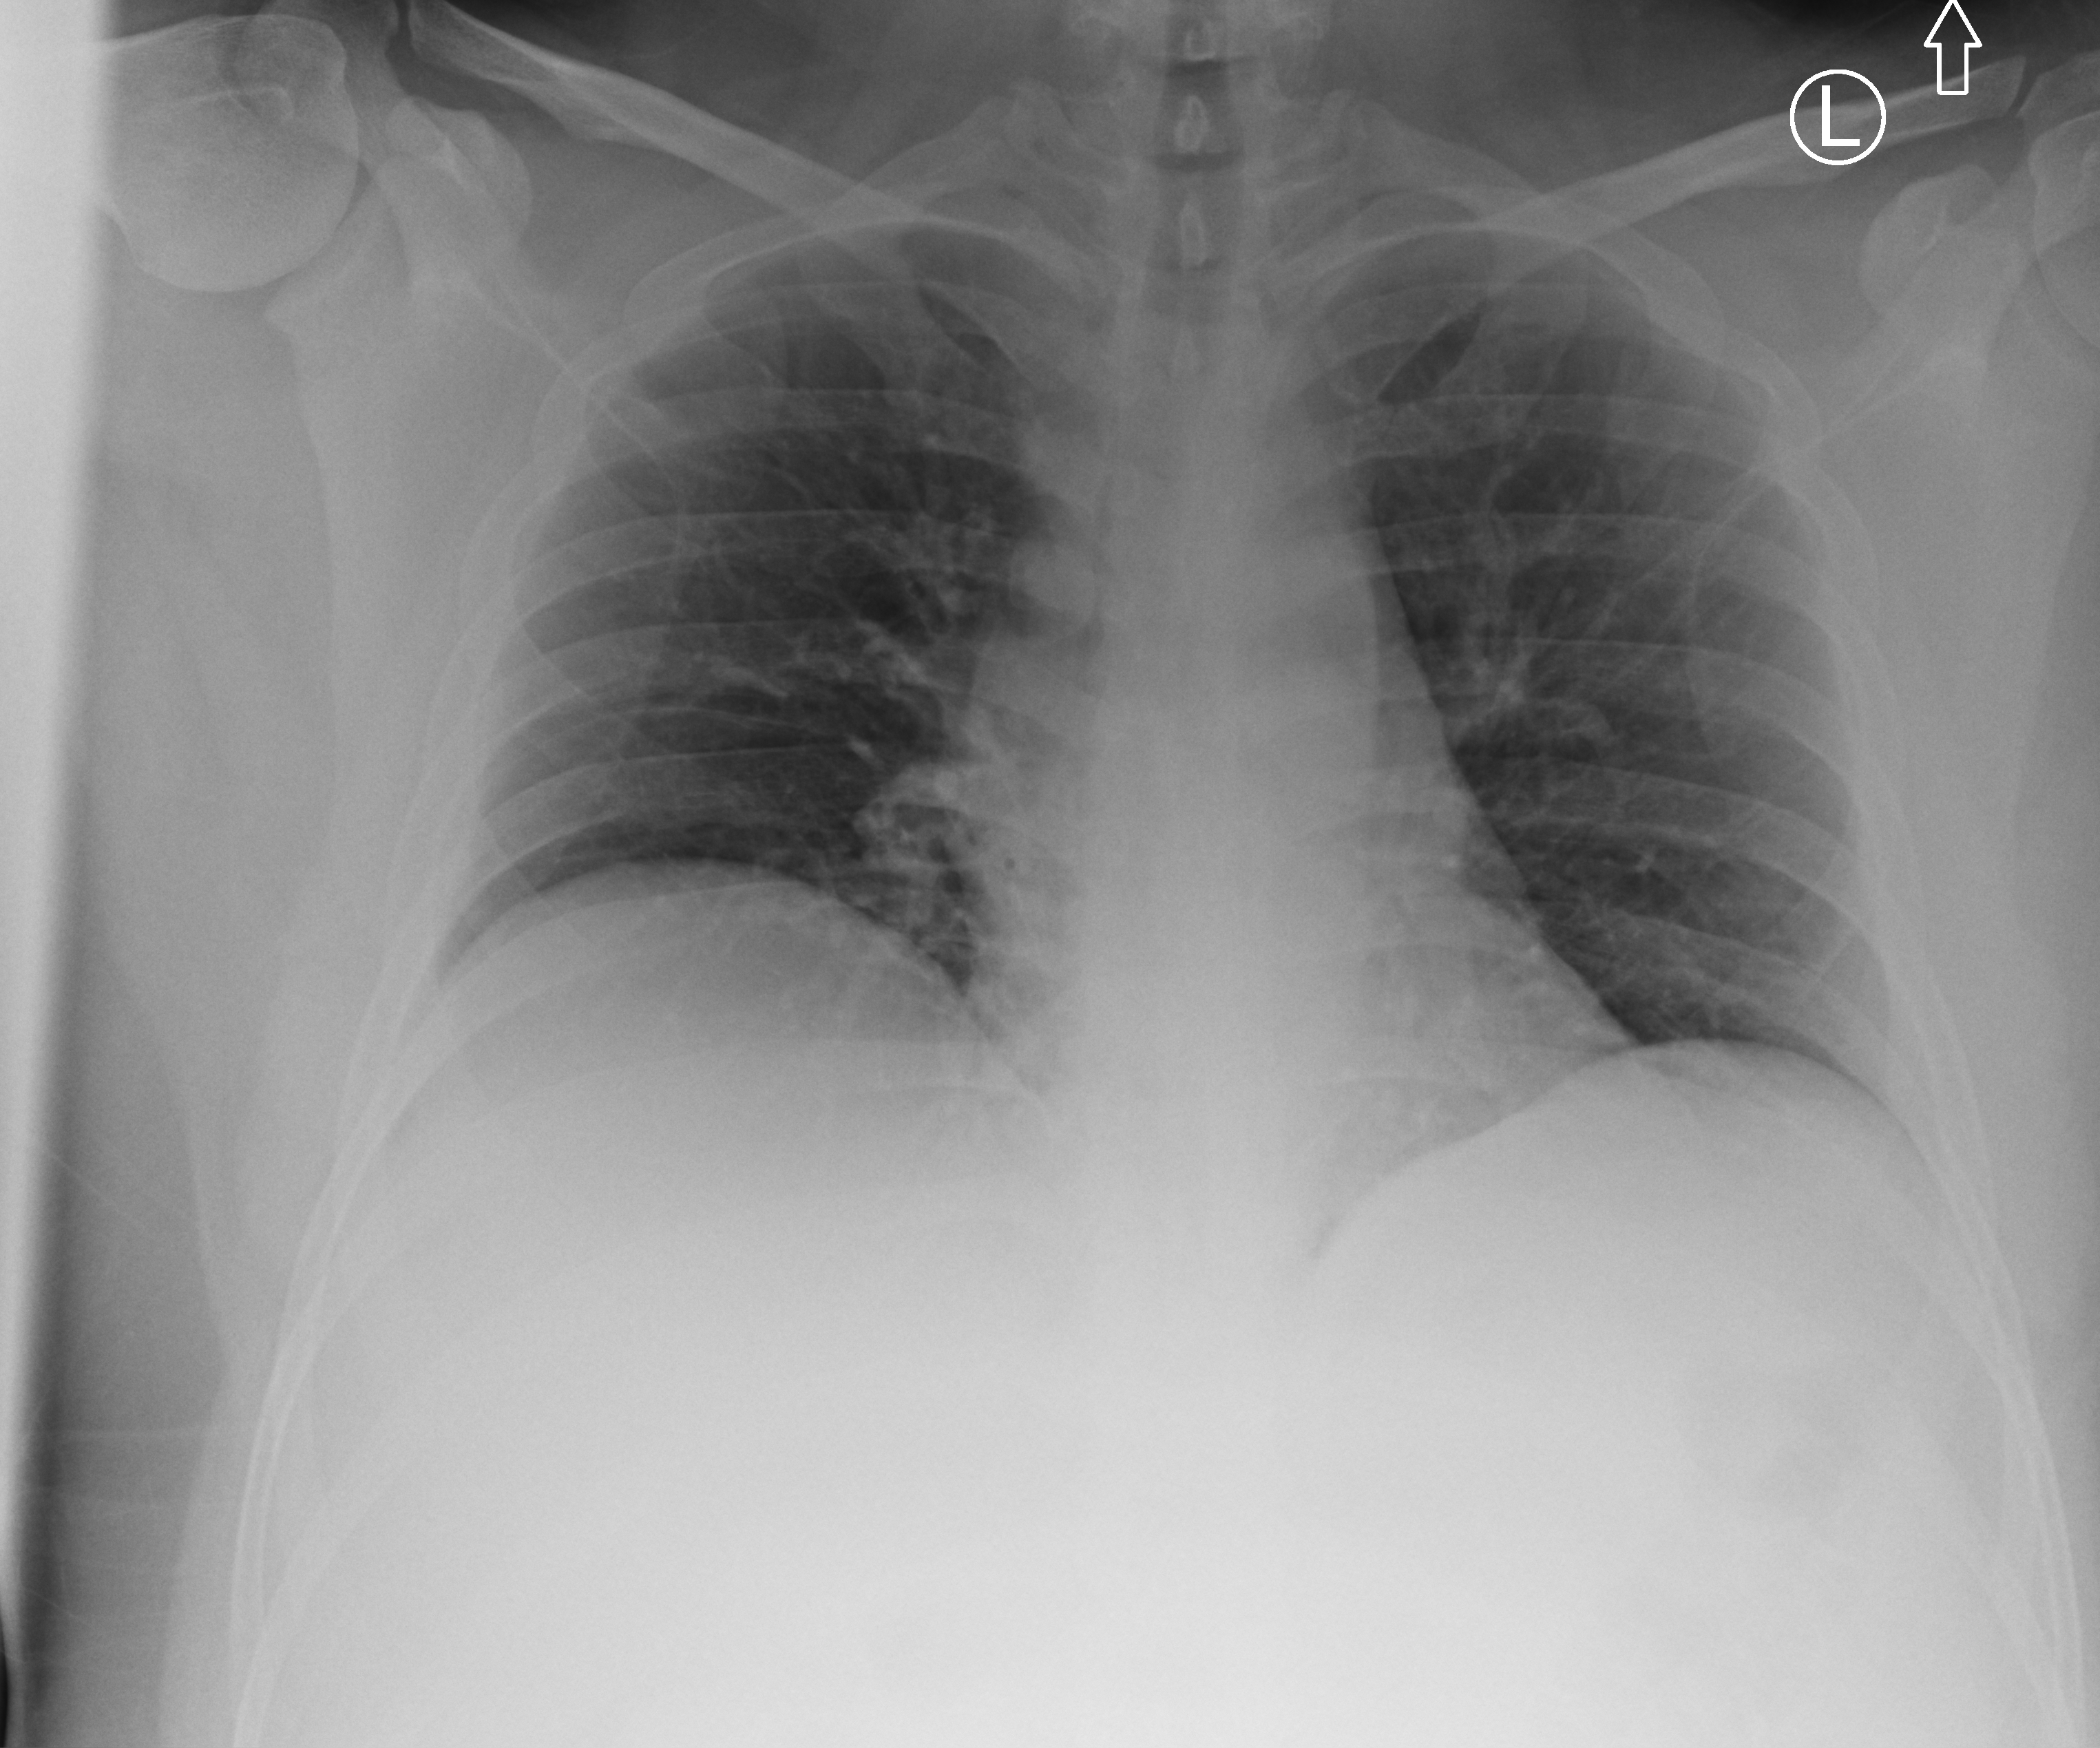
Bedside chest radiograph (computed radiography). Male patient hospitalised with COVID-19, age 18–59 years.
Hospital-stay facts (about this admission, not read from this image; timing relative to this image not recorded): admitted to intensive care during this hospital stay: no.